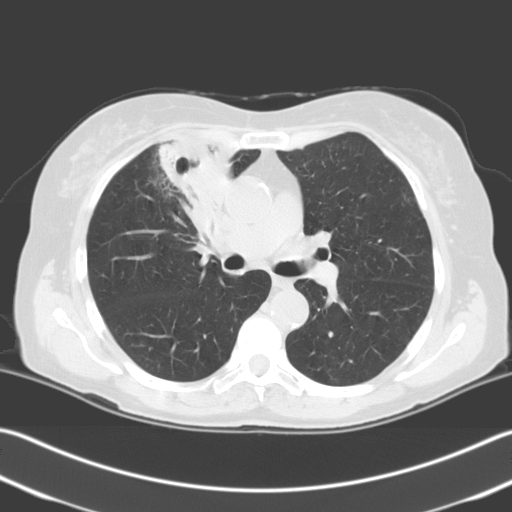
Low-dose screening chest CT, one axial slice; position 132 of 204 along the scan axis; 140 kVp; lung window (W 1500 / L -600 HU); 3.2 mm slice thickness; 512 × 512 image matrix, field of view 348 × 348 mm.
Outlined on this slice (manually delineated by an expert):
- lesion 1 (tumor, upper lobe of right lung): bounding box (x1, y1, x2, y2) in pixels: (158, 137, 236, 215)